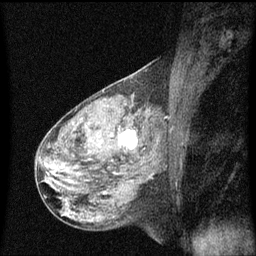
Breast MRI (dynamic contrast-enhanced), one sagittal slice. Slice 35 of 60 in the series (ordered by position). Dynamic contrast-enhanced series, image 2 of 3 at this slice position (ordered by acquisition). 1.5 T. TE 4.2 ms, TR 8 ms. 2 mm slice thickness. 256 × 256 image matrix, field of view 200 × 200 mm. Female patient, age 50 years.
Outlined on this slice (semi-automatic segmentation, software-assisted and operator-edited):
- analysis volume of interest (the breast-tissue region the enhancement analysis was run in; not a lesion): box from (x=106, y=118) to (x=148, y=159) px
- tumour enhancement mask (voxels above the 70 % enhancement threshold inside the analysis volume of interest): (x=118, y=130)–(x=137, y=149)